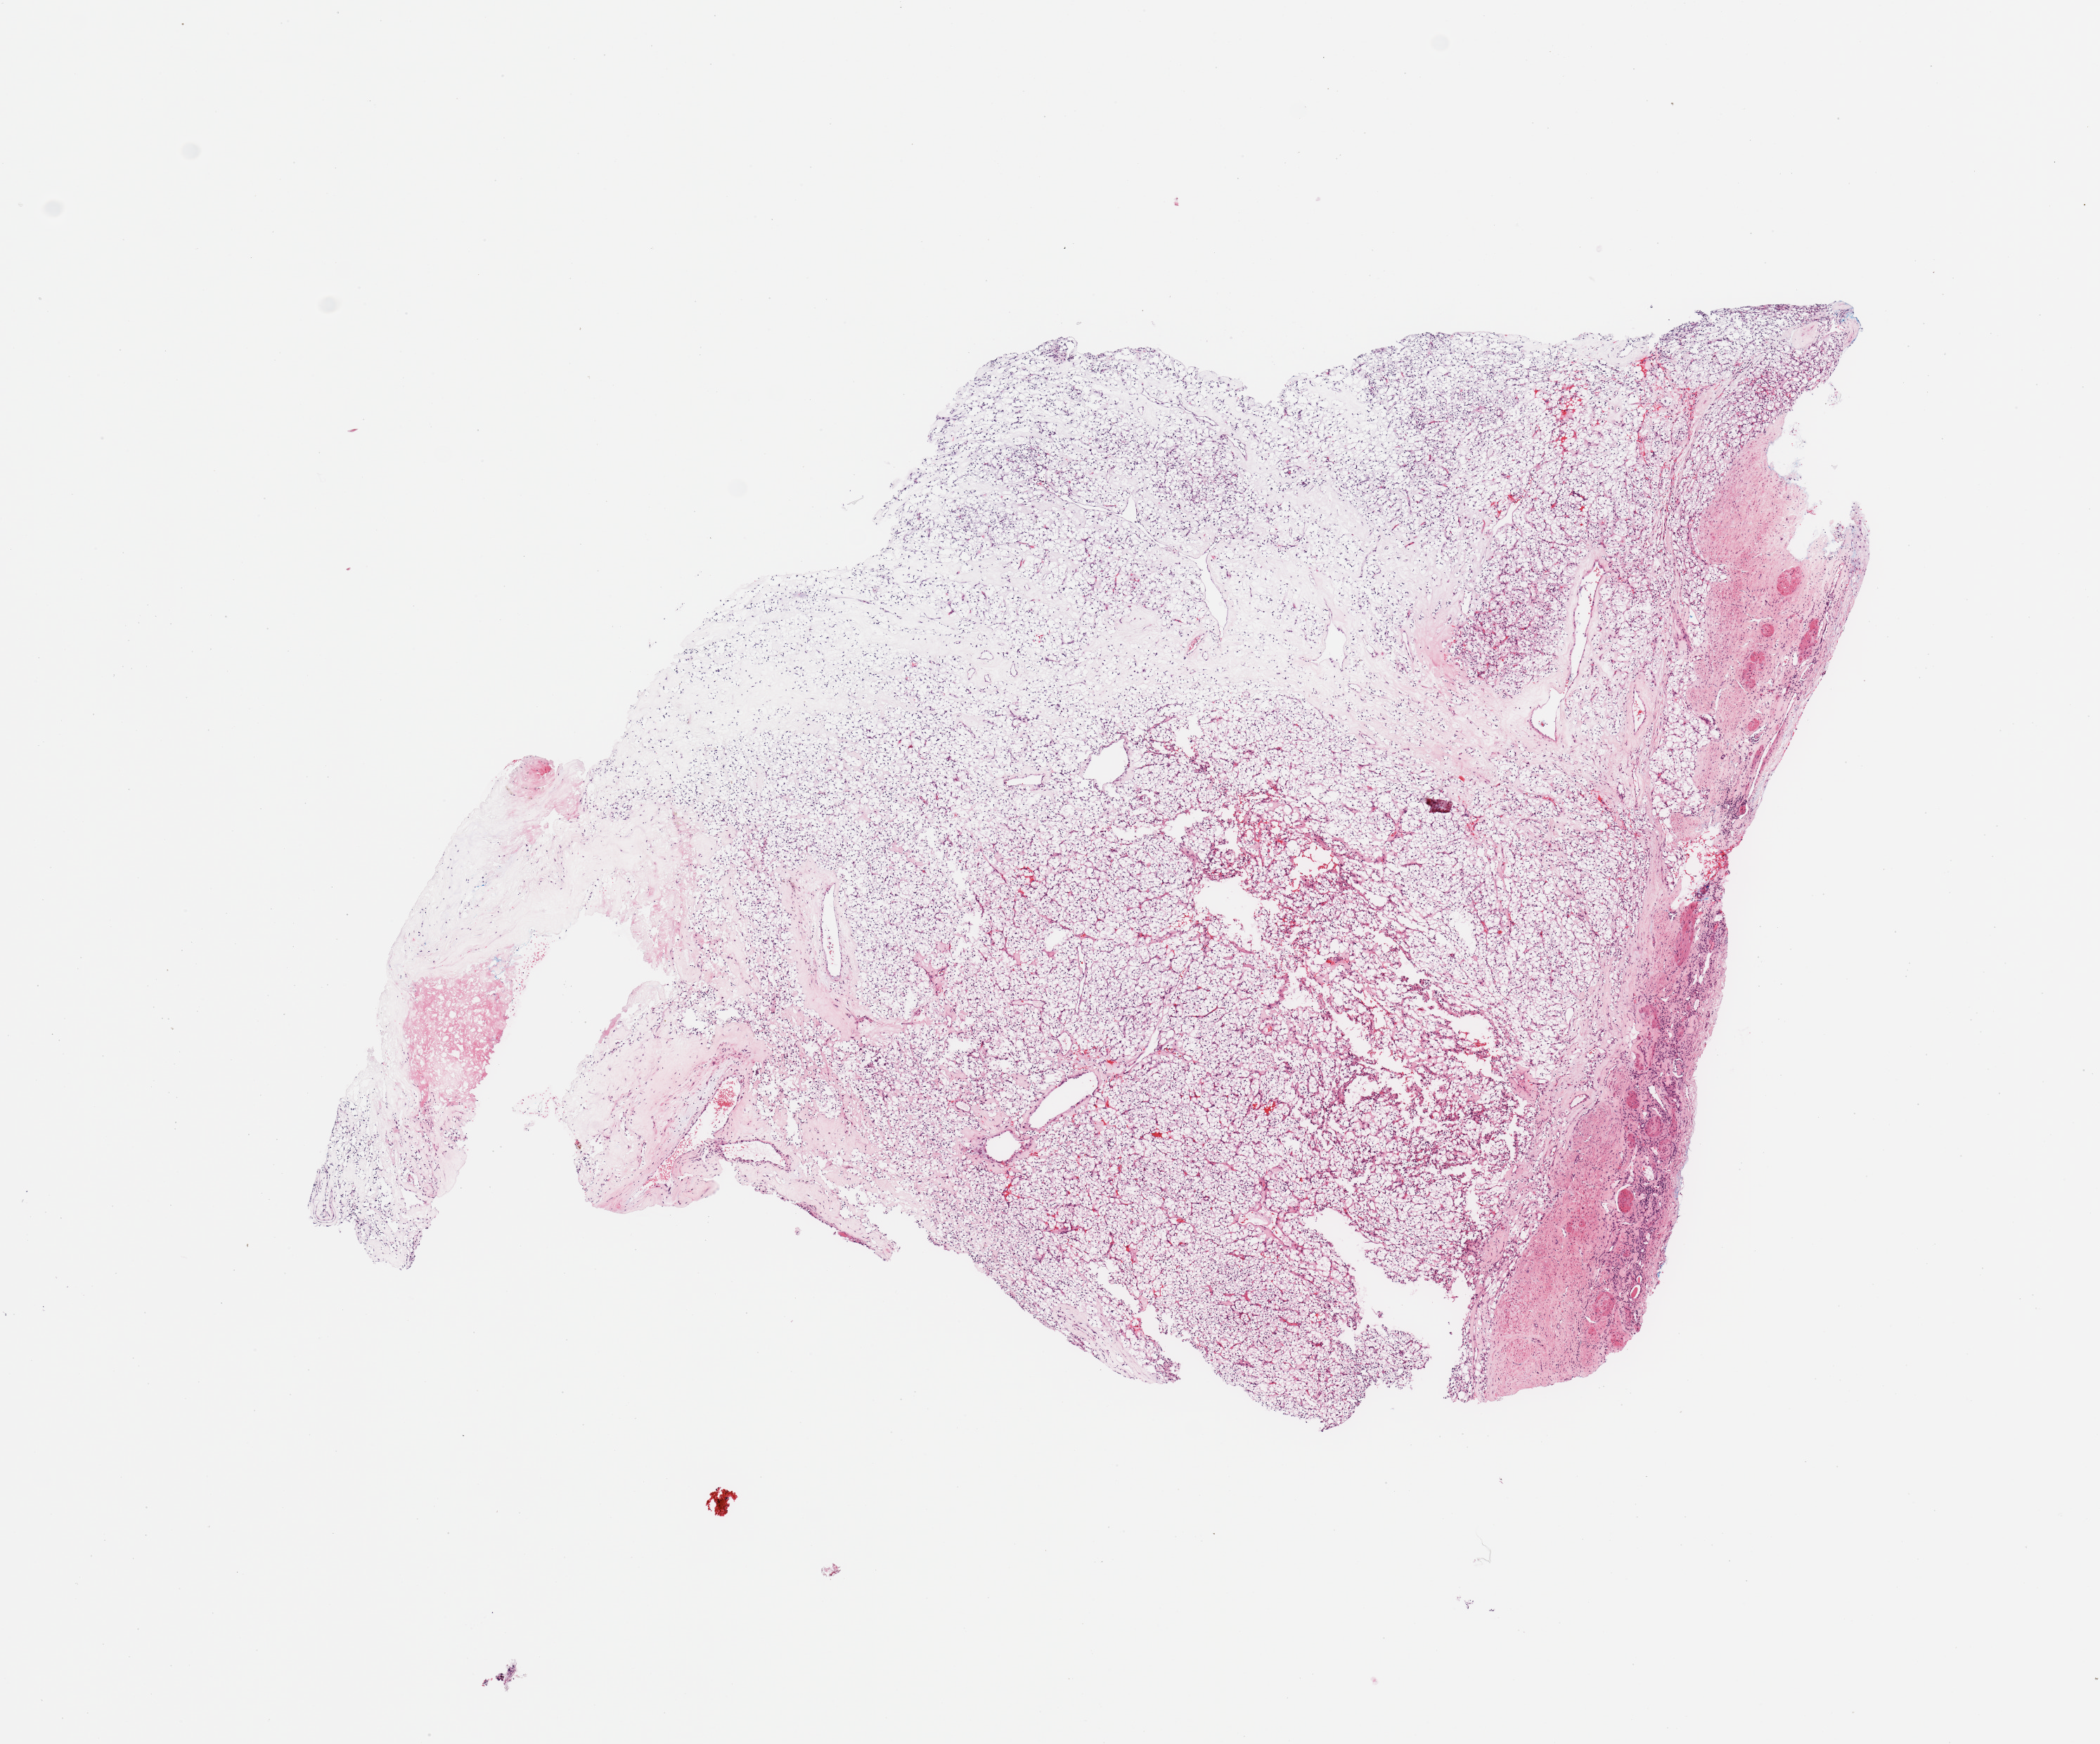
Digitized H&E-stained tissue section (whole slide) — a low-resolution overview of the entire scanned area, about 11.8 x 9.8 mm. Kidney, tumour tissue. Female, 69 y/o. Histologic grade: G1 (well differentiated).
• AJCC pathologic stage: I
• histologic diagnosis: Renal cell carcinoma, NOS
• primary tumour site (as recorded): middle